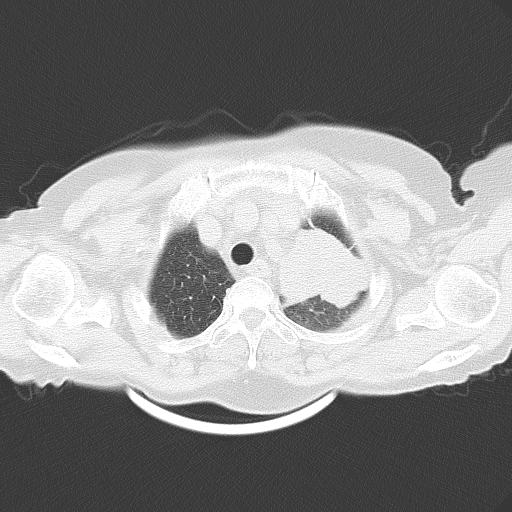
Chest CT, one axial slice; position 46 of 54 along the scan axis; reconstruction kernel B70f; 120 kVp; lung window (W 1500 / L -600 HU); 5 mm slice thickness; 512 × 512 image matrix. Patient: female, 71 years. From the clinical record (not read from this slice): clinical TNM (as recorded): T3 N3 M0.
Outlined on this slice (rectangle marked by the reading radiologist):
- lung tumour (recorded histology: adenocarcinoma): bounding box [x1, y1, x2, y2] px = [260, 213, 377, 318]